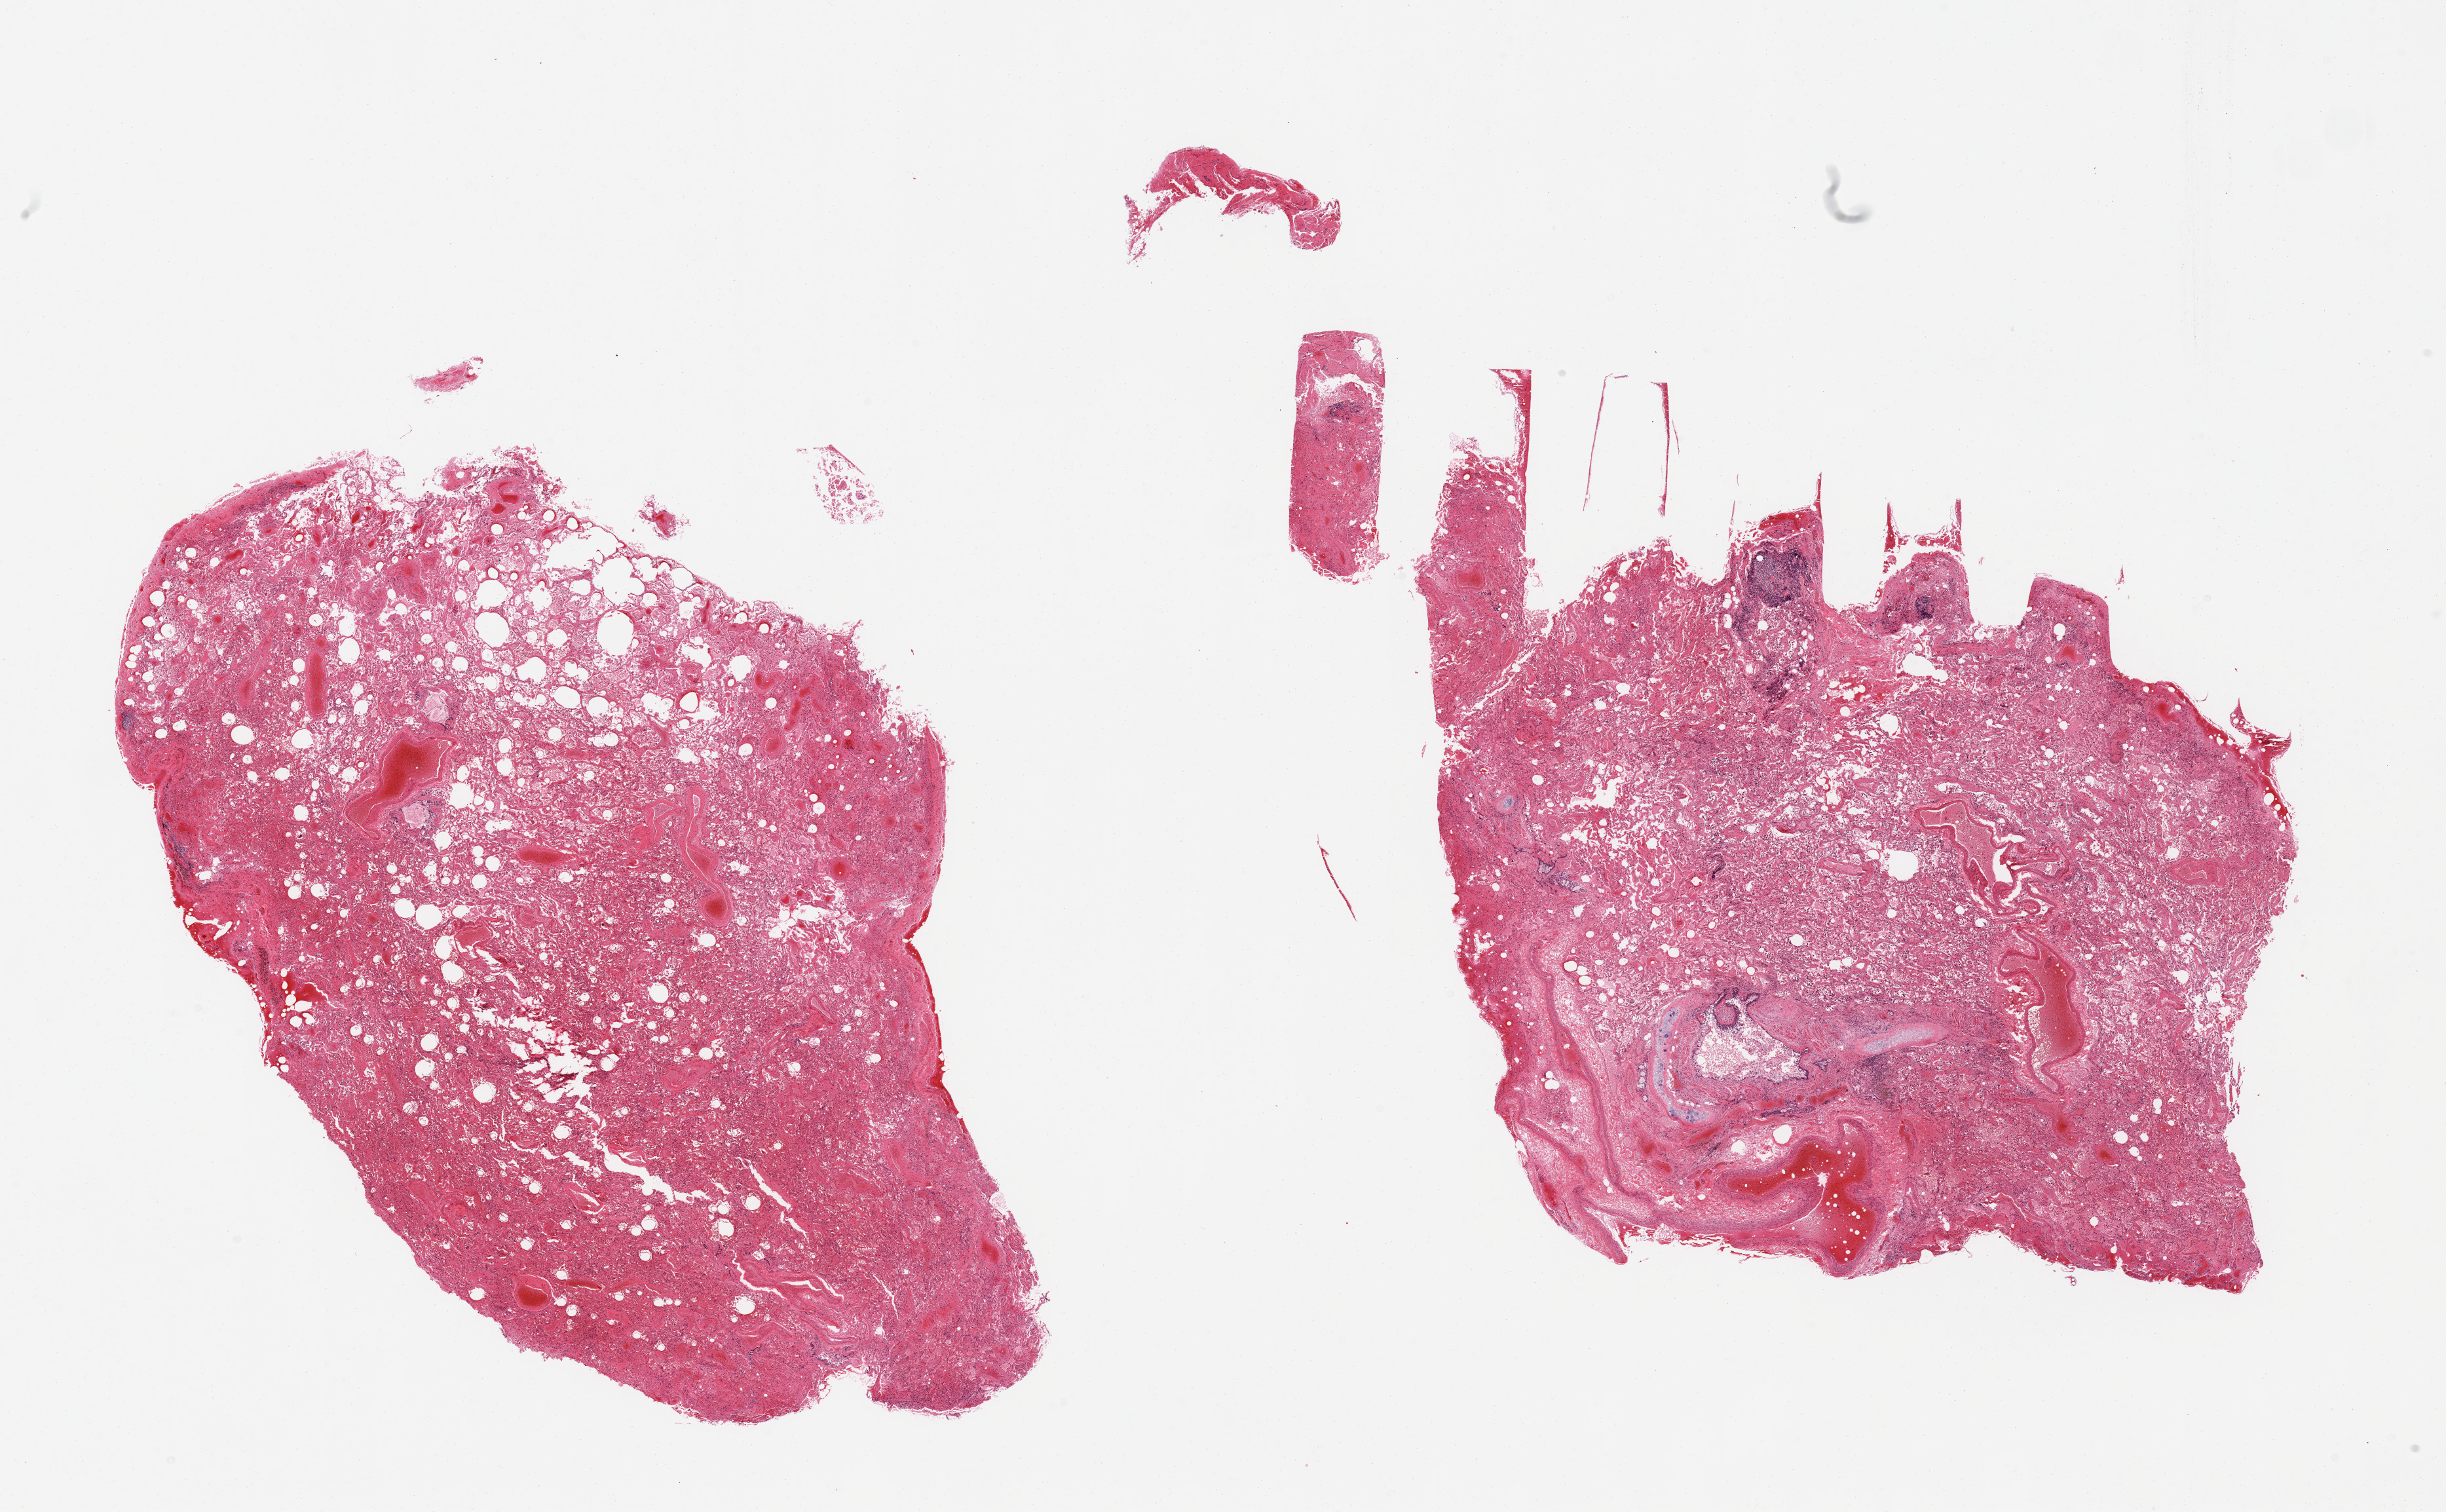
Whole-slide image, H&E stain, shown as a low-resolution overview of the whole scanned area (about 29.5 x 18.3 mm), PAXgene-fixed, paraffin-embedded tissue, target tissue: lung, donor tissue sample. Male donor.
- reviewer comment on this tissue sample: 2 pieces, several large vessels and bronchi with surrounding cartilage, hemosiderin-laden macrophages, severe congestion